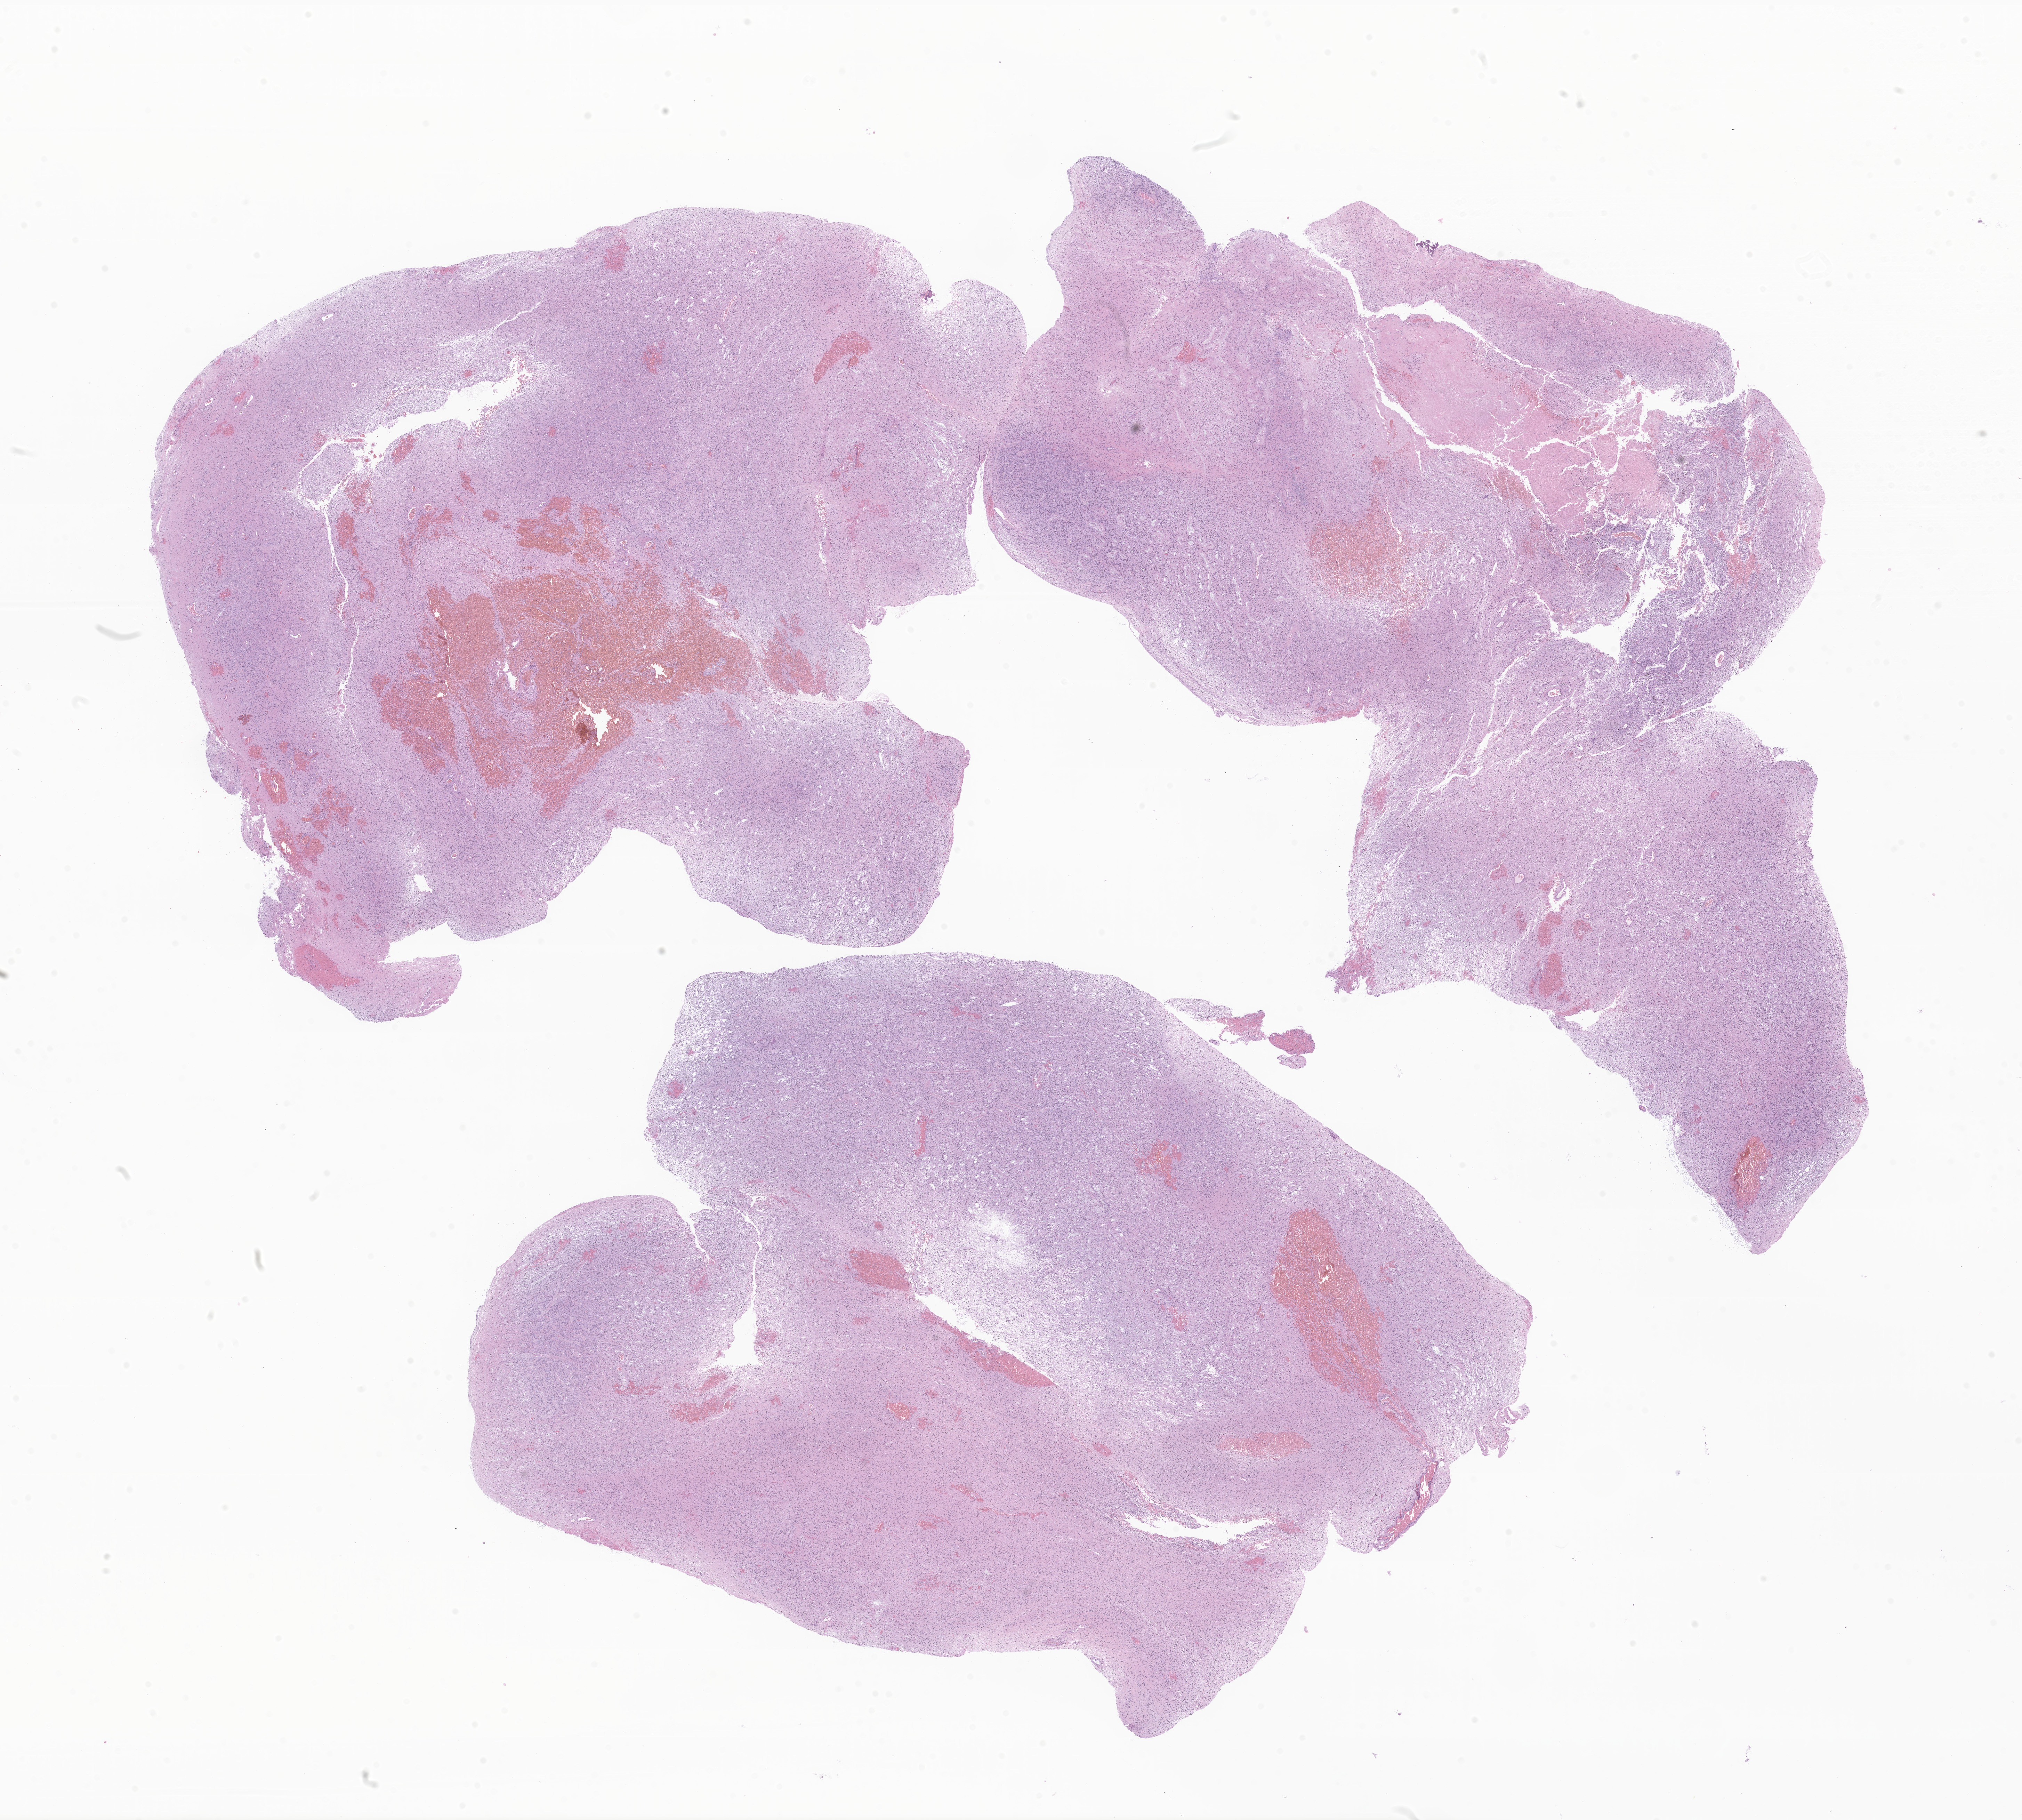
Haematoxylin and eosin whole-slide image of tumor tissue from the spinal cord, shown as a low-resolution overview of the whole scanned area (about 24.5 x 22.1 mm); formalin-fixed paraffin-embedded section. Patient male; age 101 months (8 years 5 months).
Recorded diagnosis: Pilocytic astrocytoma.